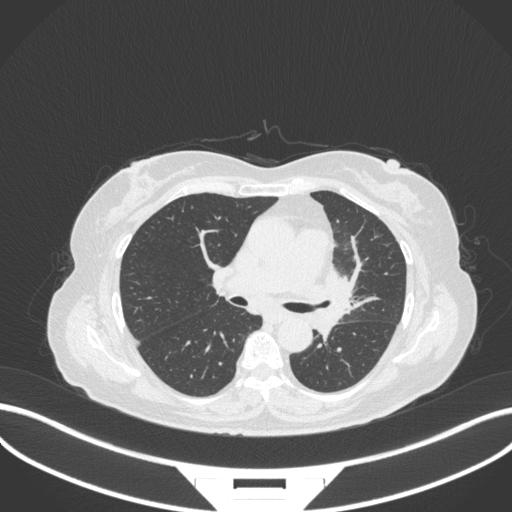
Chest CT, one axial slice. Position 194 of 382 along the scan axis. Lung window (W 1500 / L -600 HU). 1 mm slice thickness. 512 × 512 image matrix, field of view 400 × 400 mm. Female patient, age 64 years. Case-level facts recorded for this patient, not image findings: clinical TNM (as recorded): T2a N2 M0.
Outlined on this slice (bounding box drawn by a radiologist):
- lung tumour (recorded histology: adenocarcinoma): bounding box (x1, y1, x2, y2) in pixels: (320, 259, 362, 340)